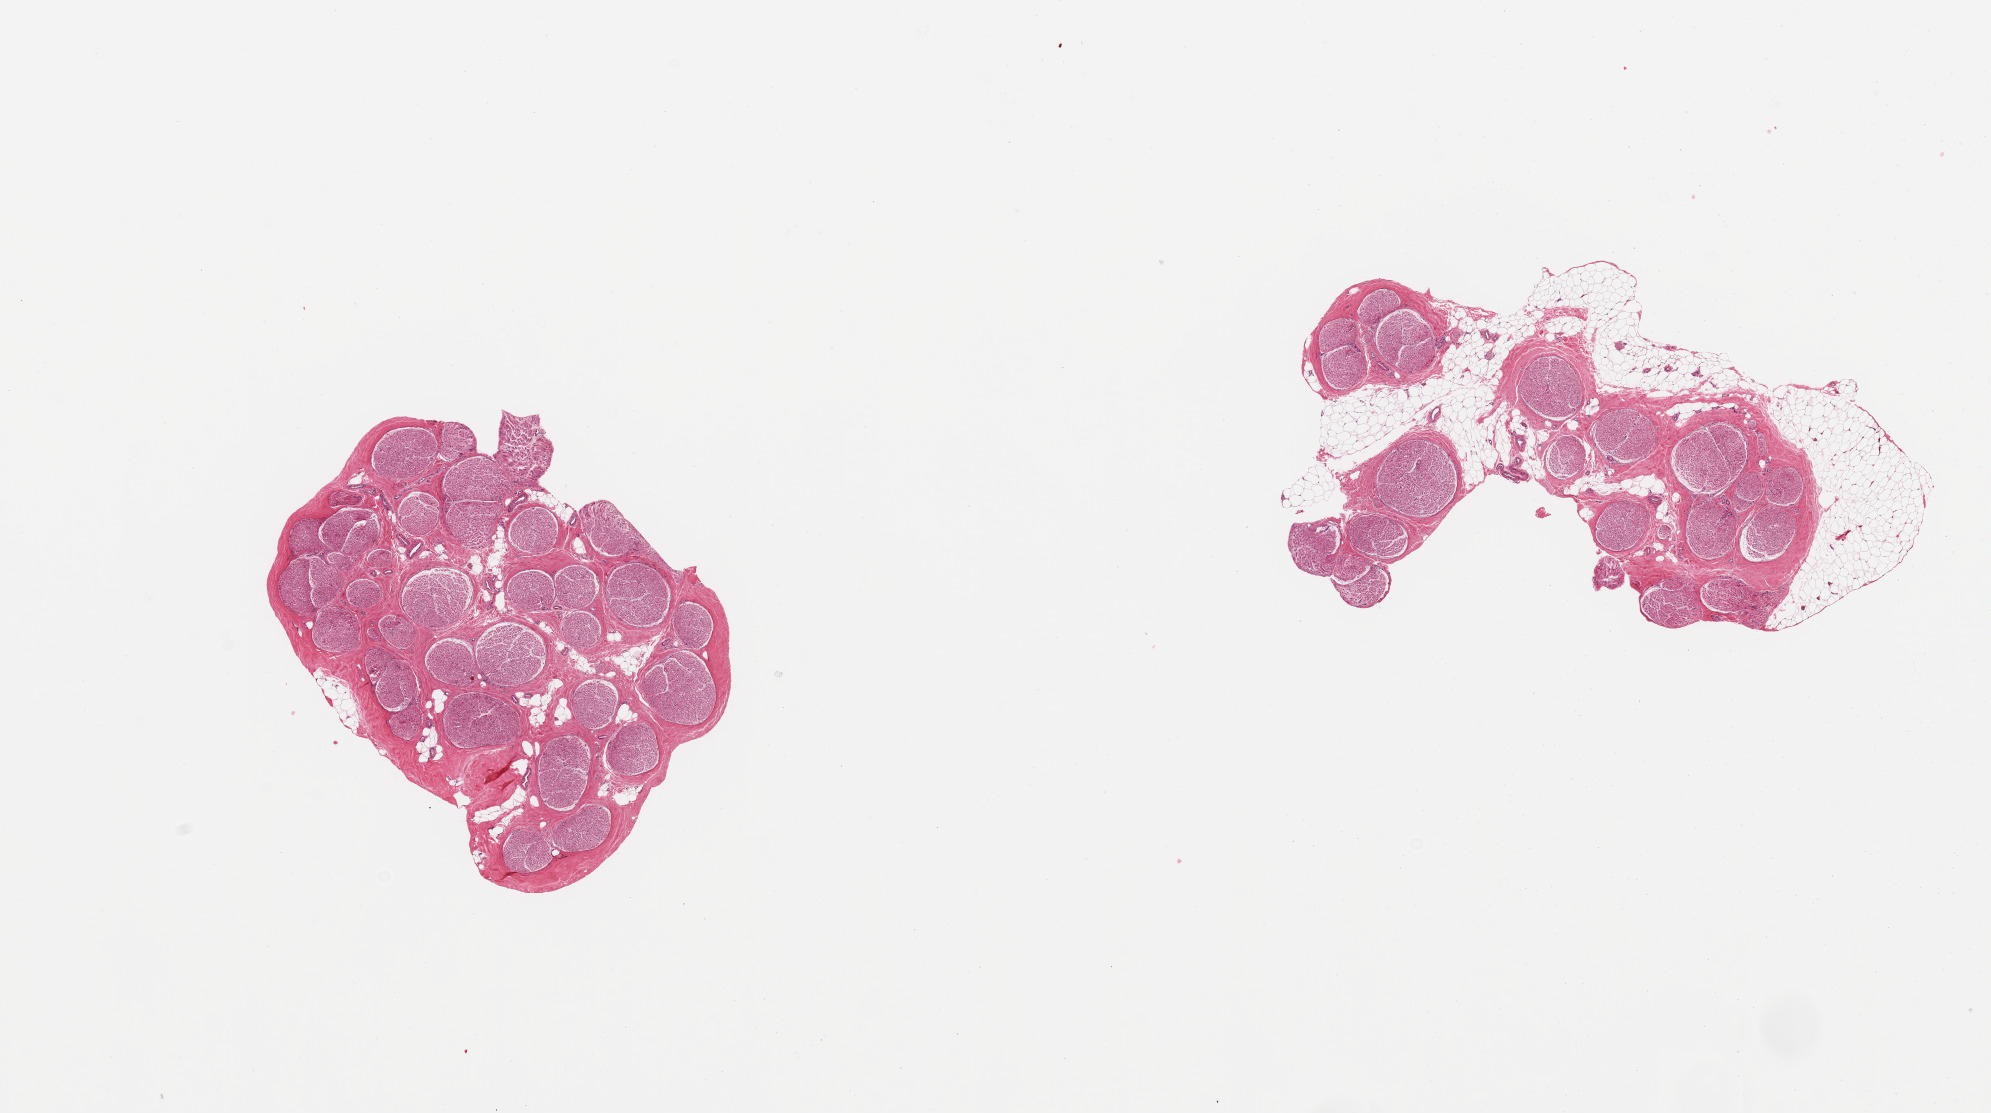
Haematoxylin and eosin whole-slide image — a low-resolution overview of the entire scanned area, about 15.8 x 8.8 mm (slide scanned at 20x), PAXgene-fixed, paraffin-embedded tissue, section of tibial nerve (target tissue), donor tissue sample. Male donor.
• pathologist's review note for this sample: 2 pieces, nubbin of adherent fat, up to ~0.8mm